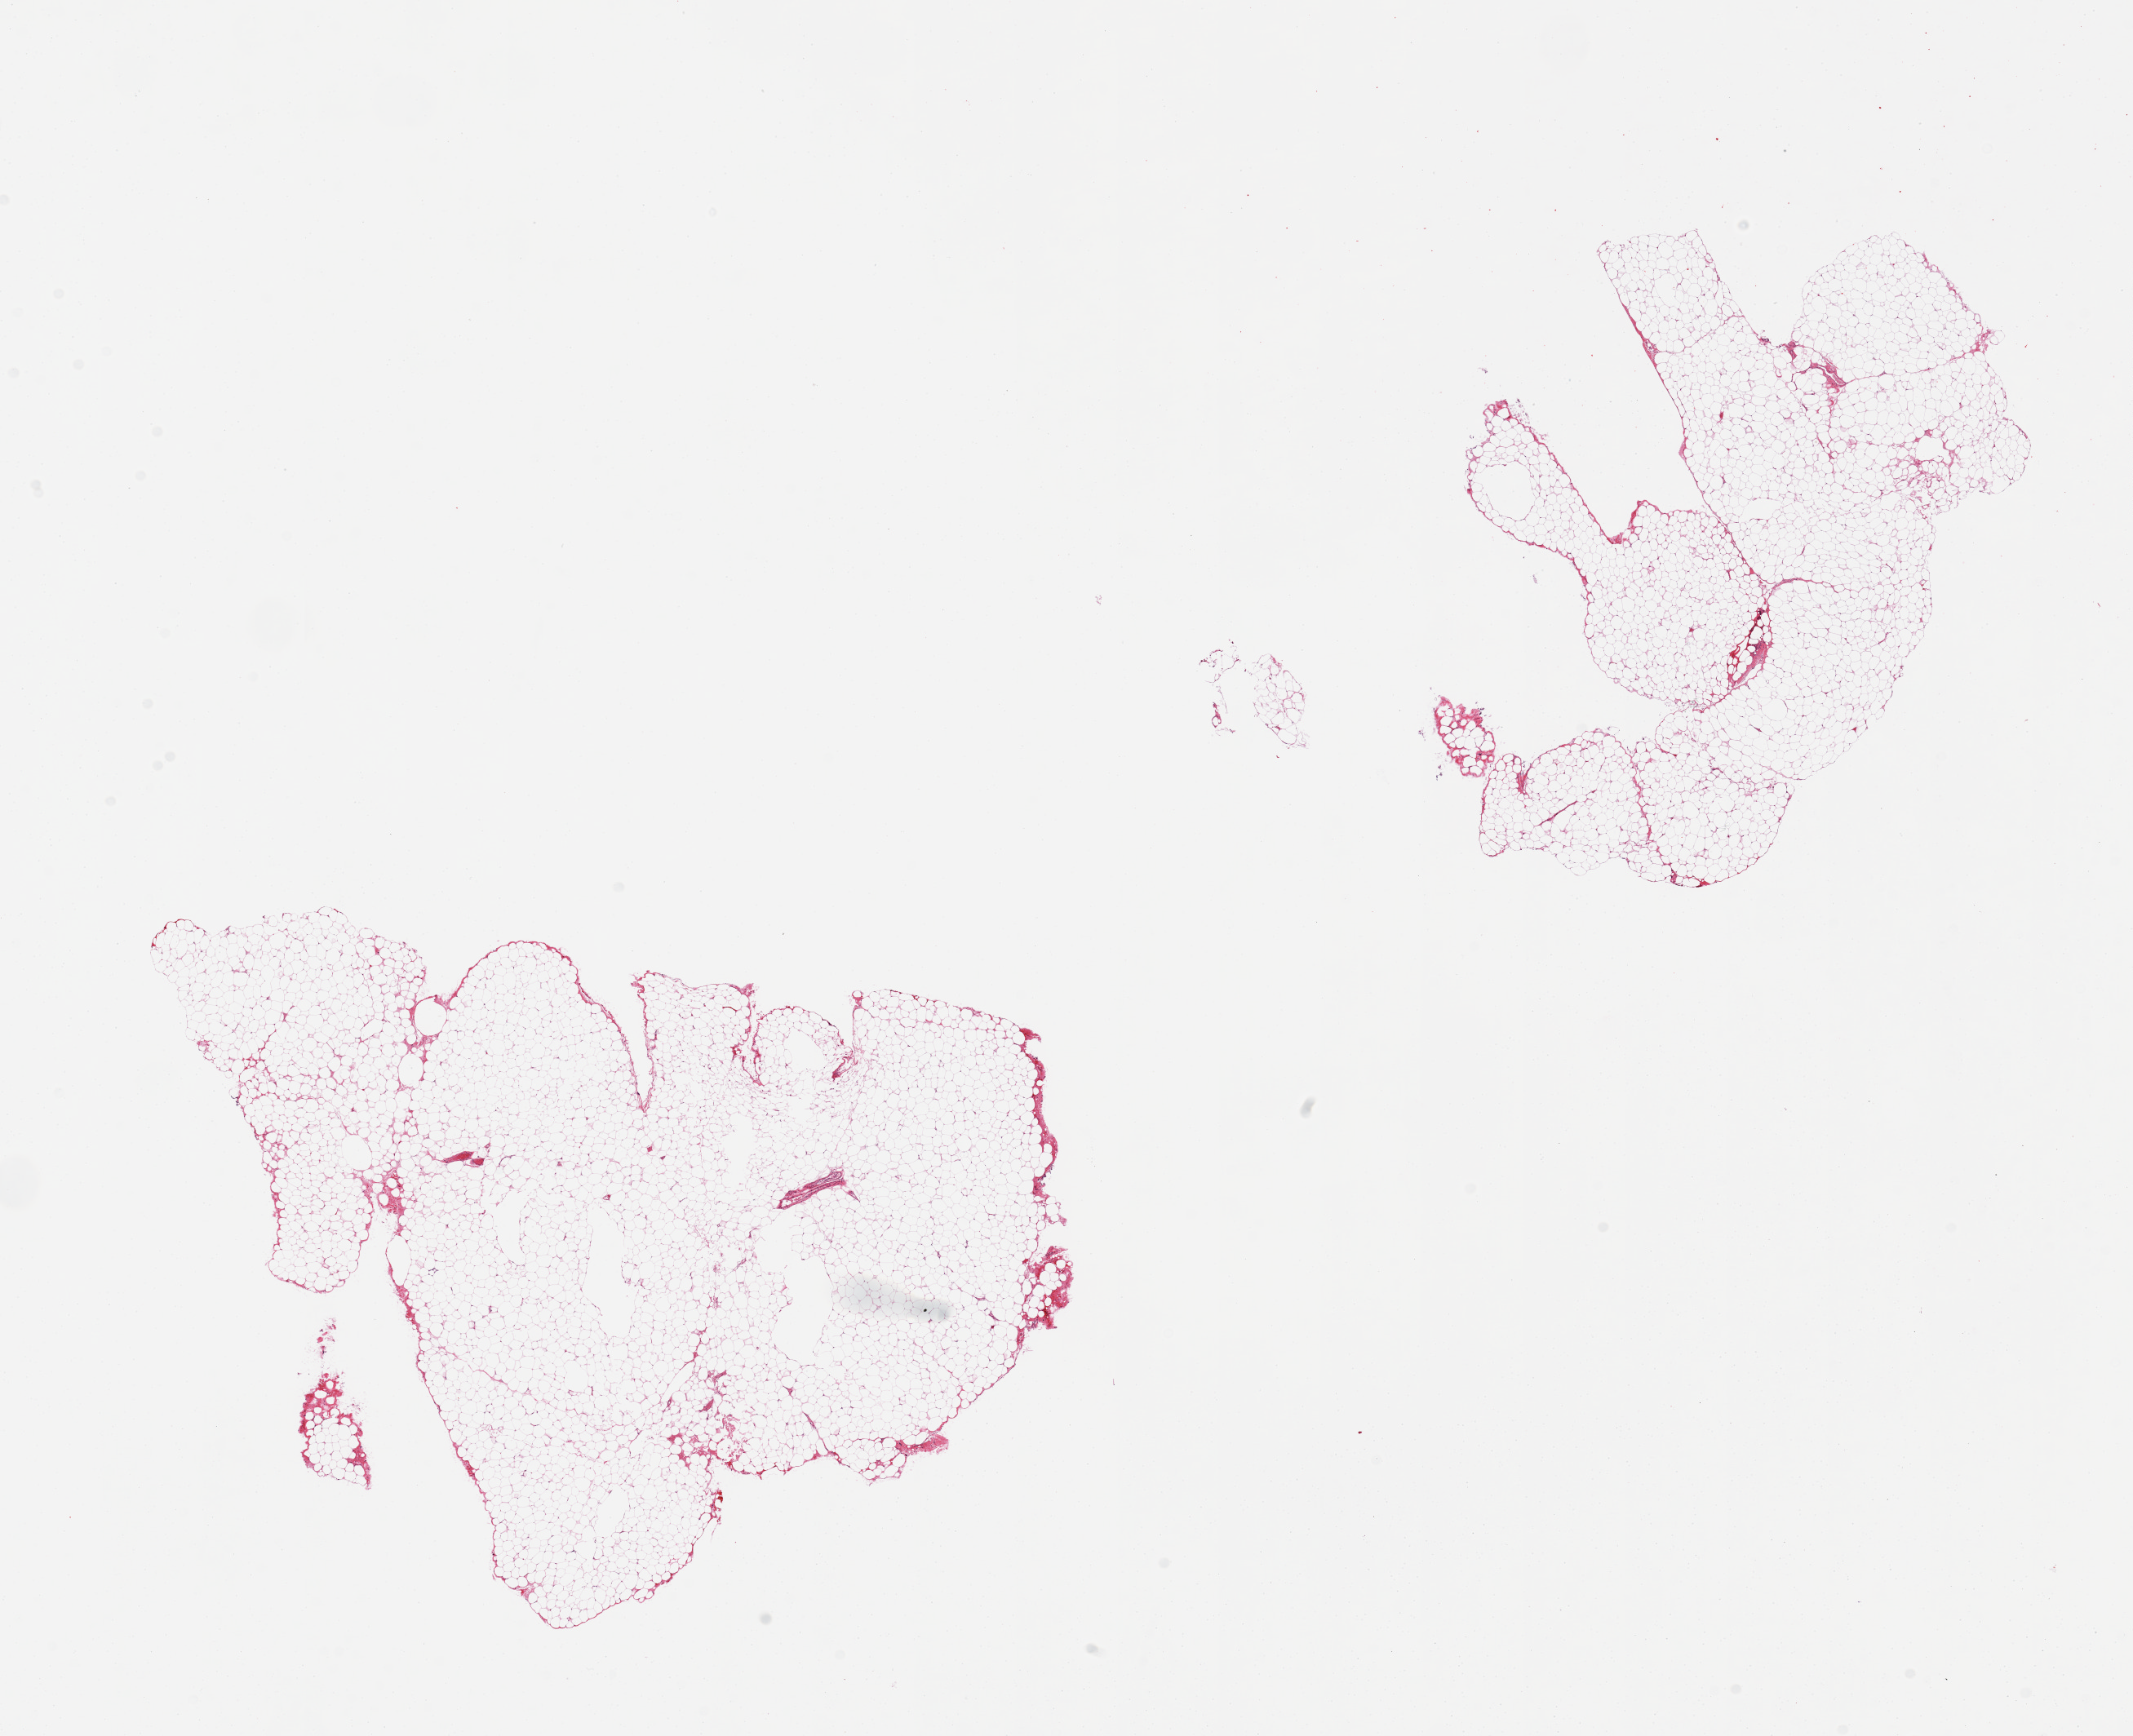
Haematoxylin and eosin whole-slide image, brightfield — a low-resolution overview of the entire scanned area, about 20.7 x 16.8 mm, PAXgene-fixed, paraffin-embedded tissue, section of omentum (target tissue), tissue donor sample. Donor: female.
Reviewer comment on this tissue sample: 2 pieces.